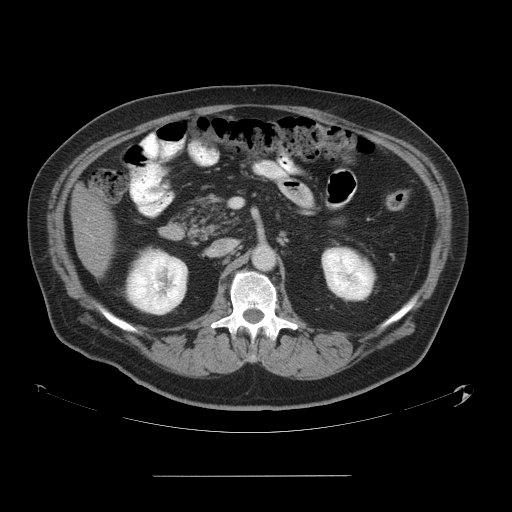
Contrast-enhanced abdominal CT, one axial slice. Position 23 of 58 along the scan axis. 120 kVp. Soft-tissue window (W 400 / L 40 HU). 5 mm slice thickness. 512 × 512 image matrix, field of view 480 × 480 mm. Male patient, age 63 years. Case-level facts recorded for this patient, not image findings: diagnosis: colorectal cancer liver metastases, imaged before liver resection; multiple liver metastases: no; largest metastasis: 4.2 cm.
Annotated regions visible in this slice (expert manual segmentation):
- liver: bounding box (x1, y1, x2, y2) in pixels: (72, 188, 112, 273)
- planned liver remnant (the part of the liver to remain after resection): (72, 188, 113, 273)